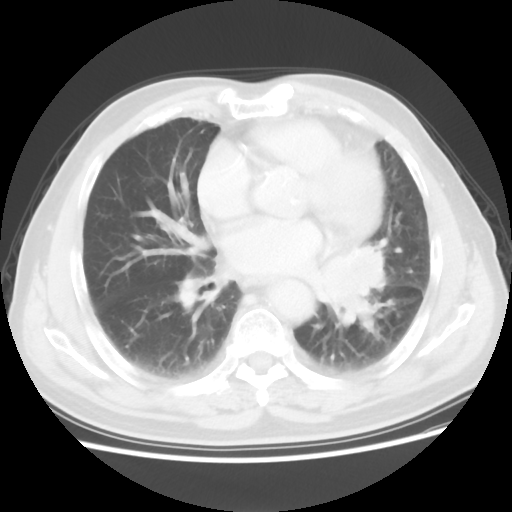
Chest CT, one axial slice. Position 28 of 56 along the scan axis. 120 kVp. Lung window (W 1500 / L -600 HU). 5 mm slice thickness. 512 × 512 image matrix, field of view 360 × 360 mm. Male patient, age 75 years. From the clinical record (not read from this slice): clinical TNM (as recorded): T3 N0 M0.
Structures marked on this image (rectangle marked by the reading radiologist):
- lung tumour (recorded histology: squamous cell carcinoma): bounding box (x1, y1, x2, y2) in pixels: (311, 242, 399, 326)